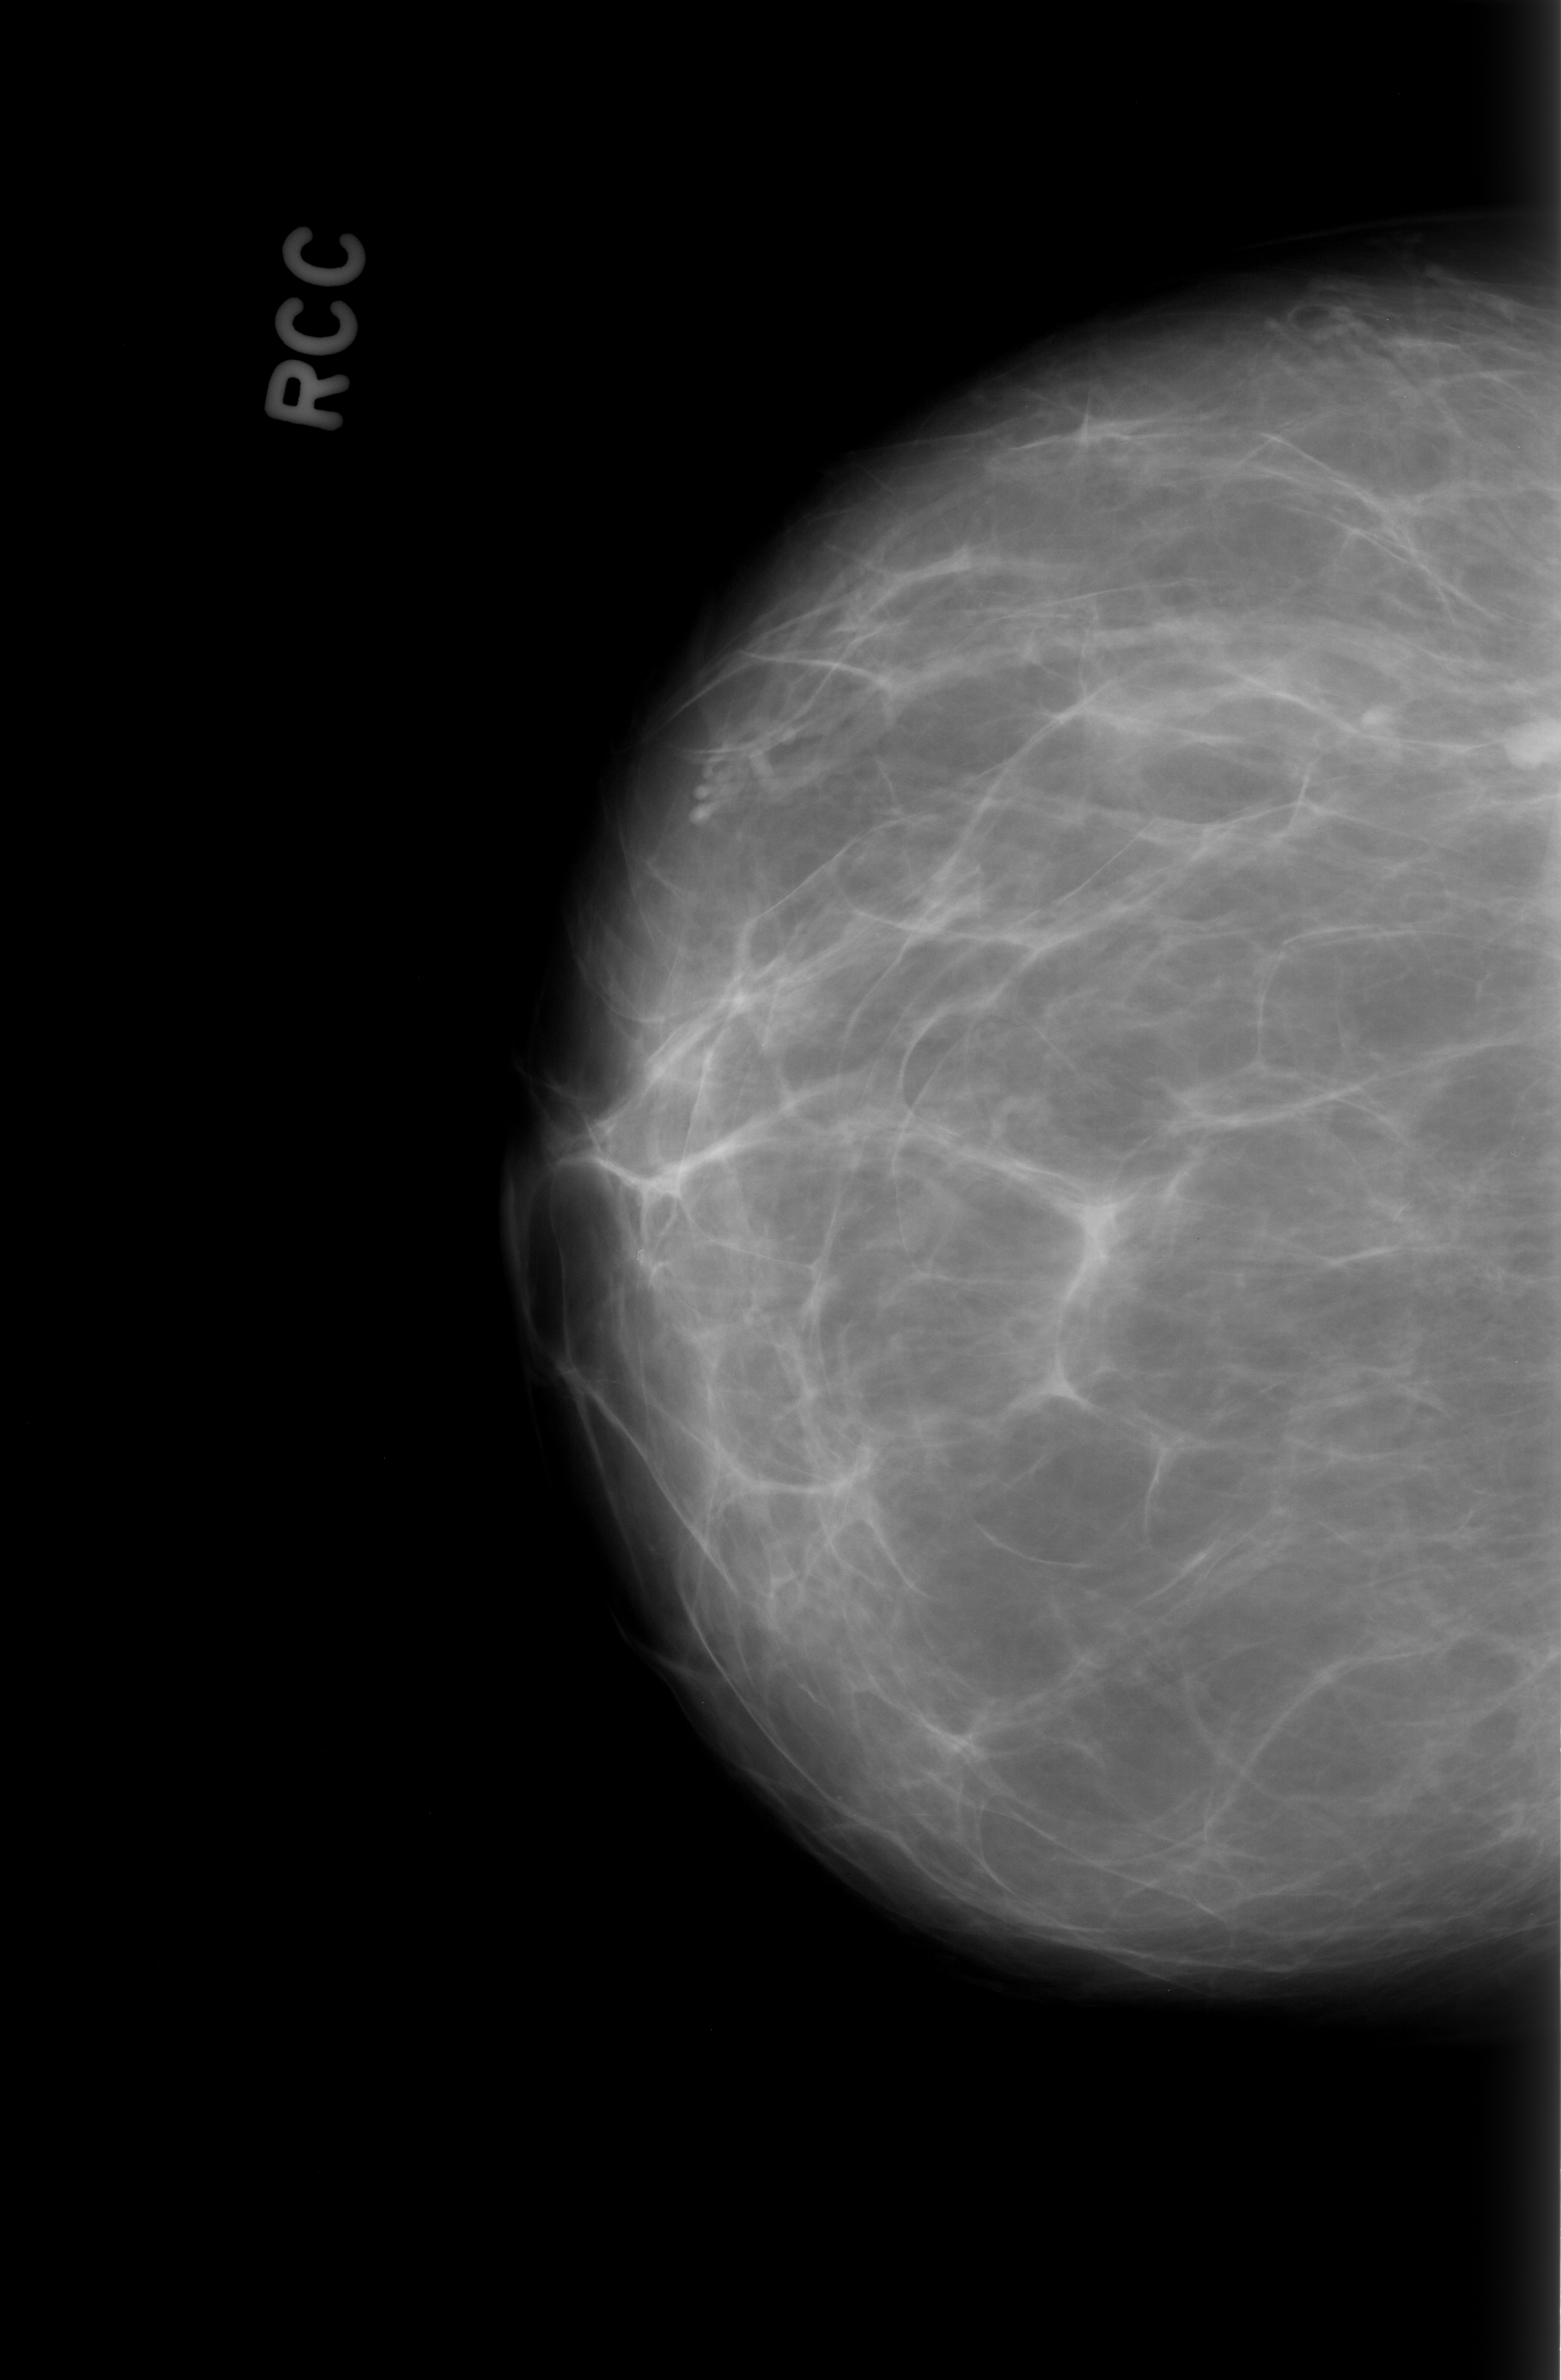
Scanned film-screen mammogram, right breast, craniocaudal (CC) view.
Marked findings (only marked abnormalities are described; nothing is implied about the rest of the image): mass, shape lobulated, margins circumscribed; BI-RADS assessment category 3; subtlety rating 5 on a 1 (subtle) to 5 (obvious) scale; benign; no additional work-up was recommended (benign without callback).